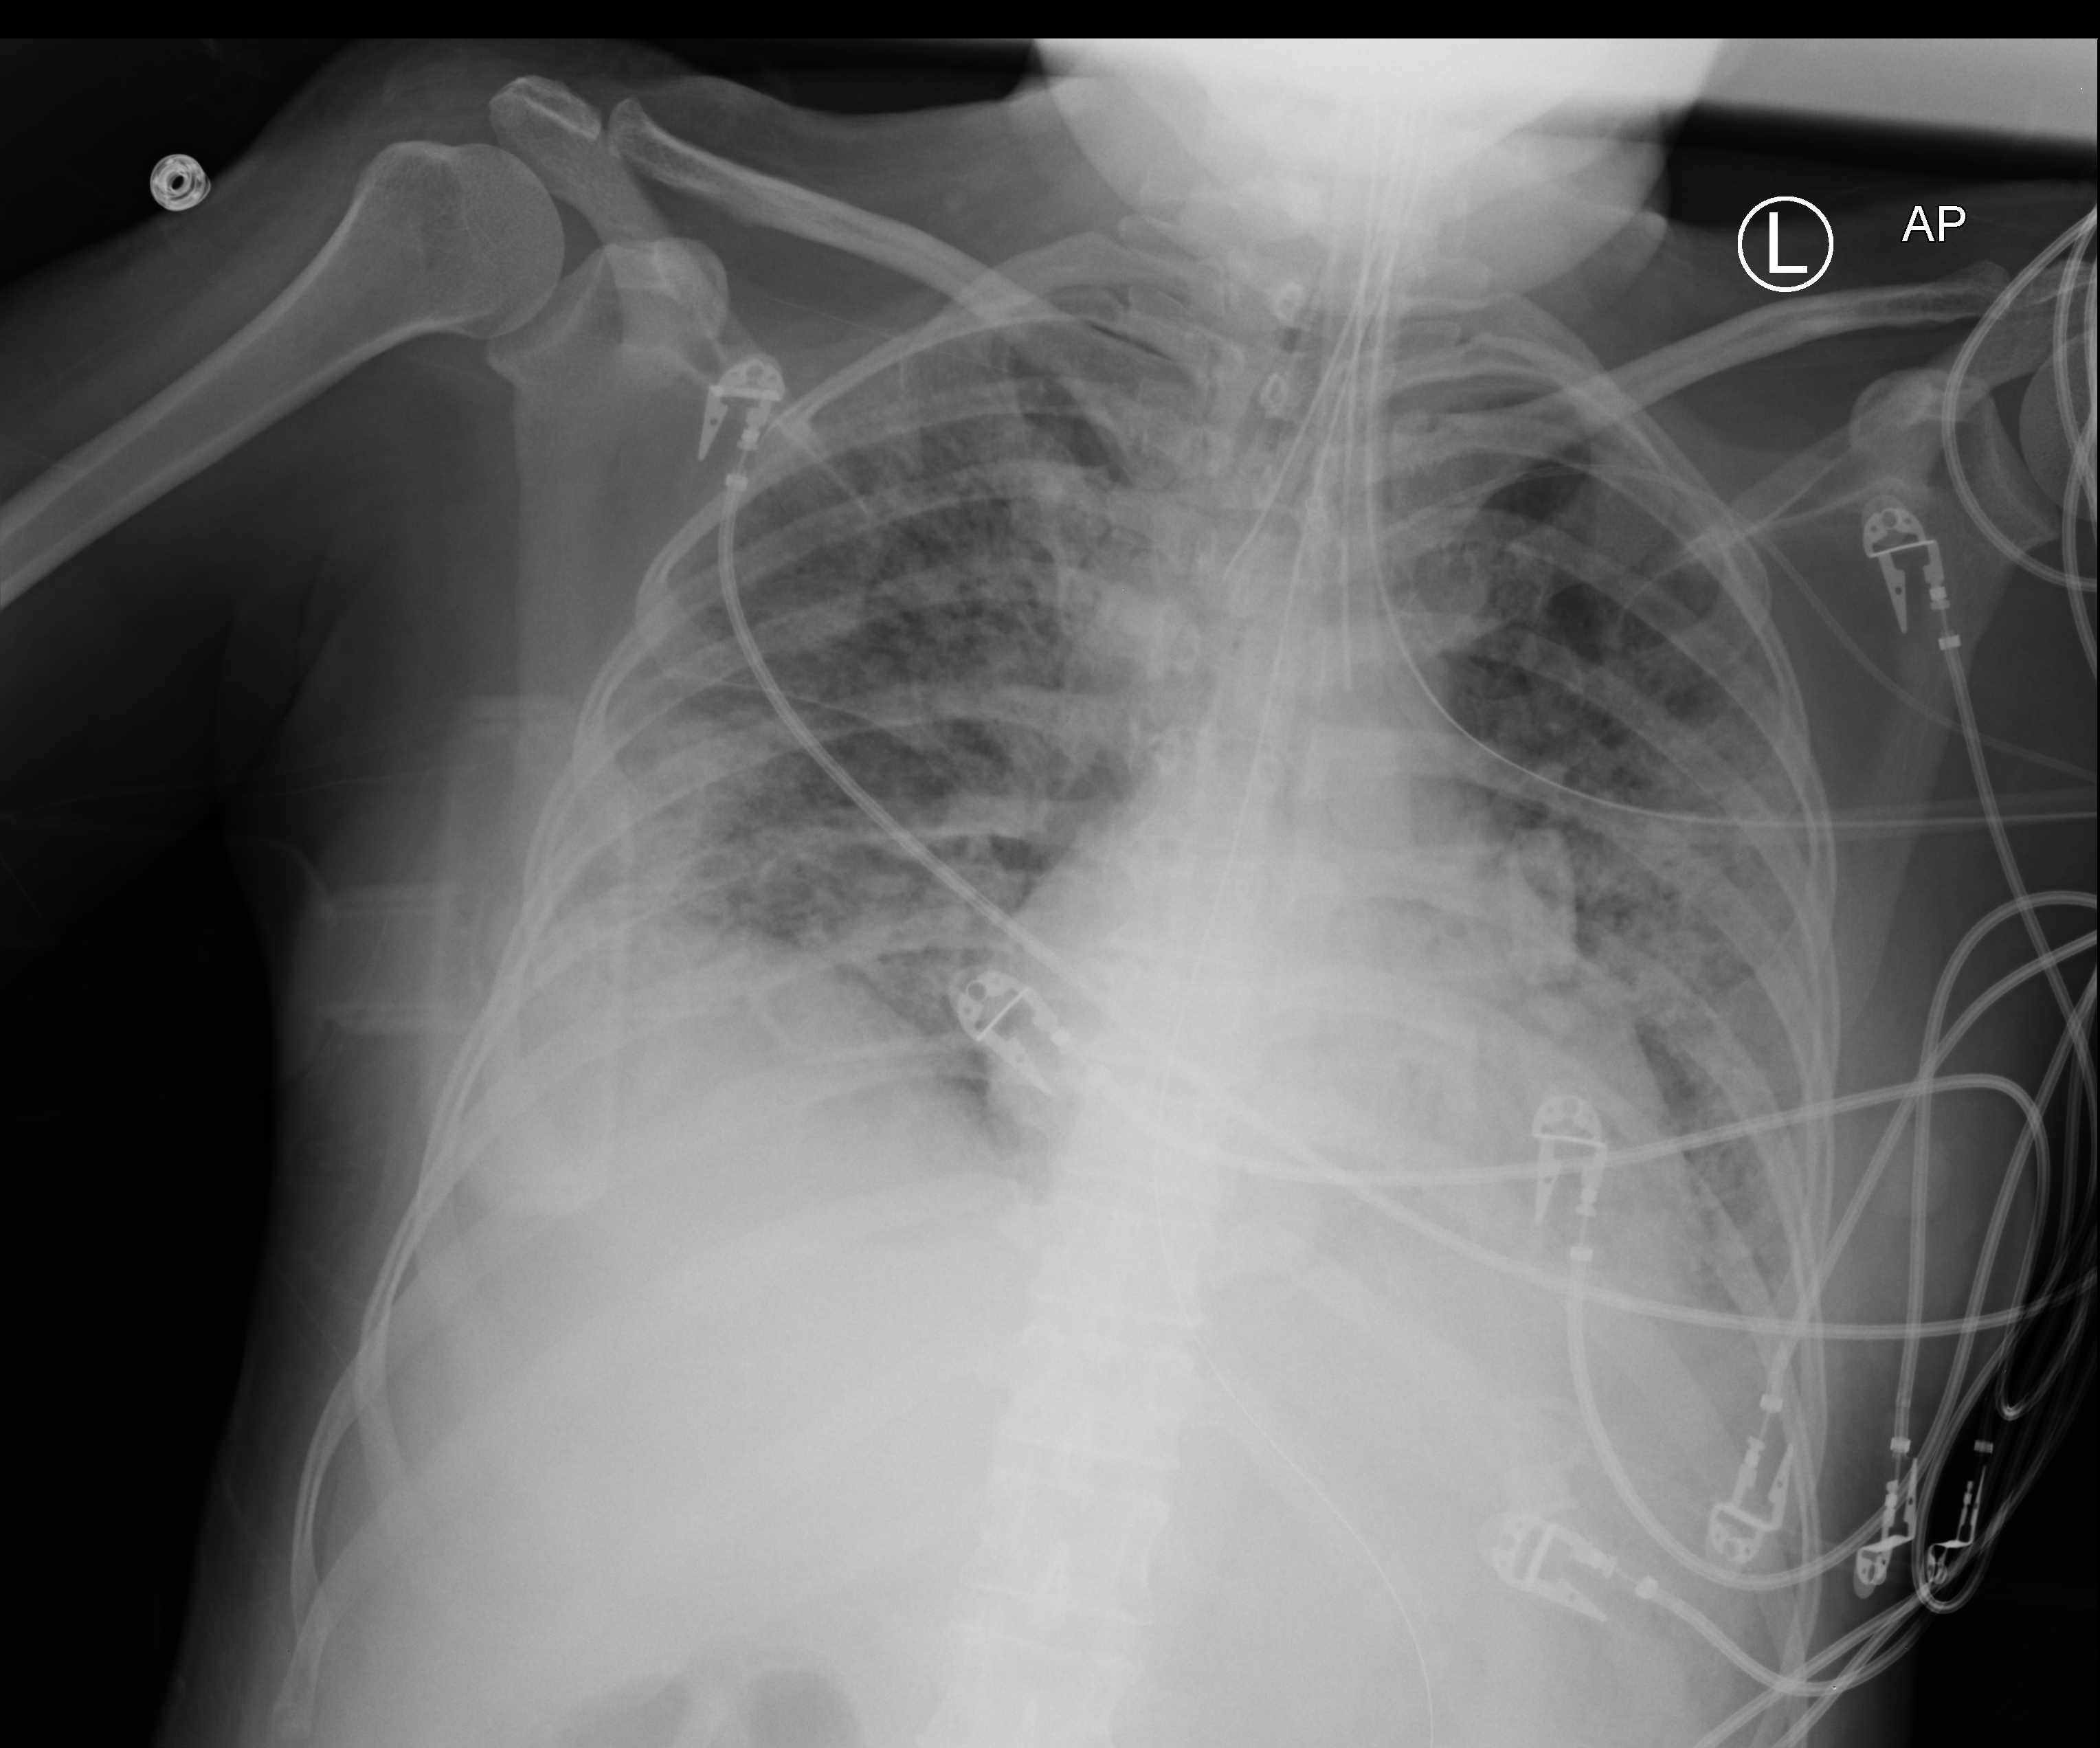
Portable chest radiograph; anteroposterior (AP) projection. Female patient hospitalised with COVID-19, age 18–59 years.
From the hospital-stay record, not from the radiograph (when in the stay this image was taken is not recorded): length of hospital stay: 71 days; admitted to intensive care during this hospital stay: yes; chronic kidney disease (admission record): no.